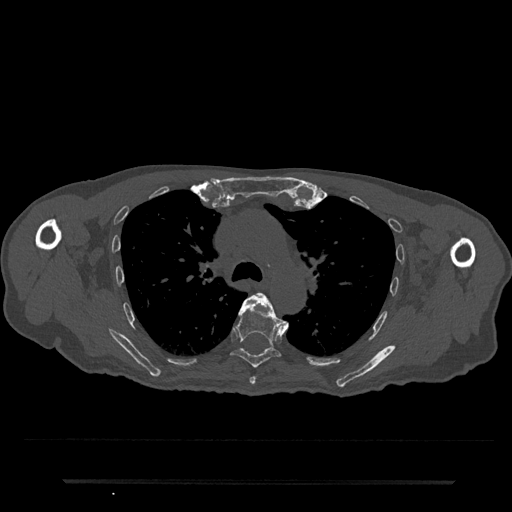
CT including the spine, one axial slice. Slice 538 of 797 in the series (ordered by position). 120 kVp. Bone window (W 1800 / L 400 HU). 512 × 512 image matrix. Male patient, age 74 years. From the clinical record (not read from this slice): primary cancer: prostate.
Outlined on this slice (semi-automatic segmentation, software-assisted and operator-edited):
- T5 vertebra: bounding box <249,293,289,385> (left, top, right, bottom; pixels)
- T6 vertebra: <231,294,281,368>